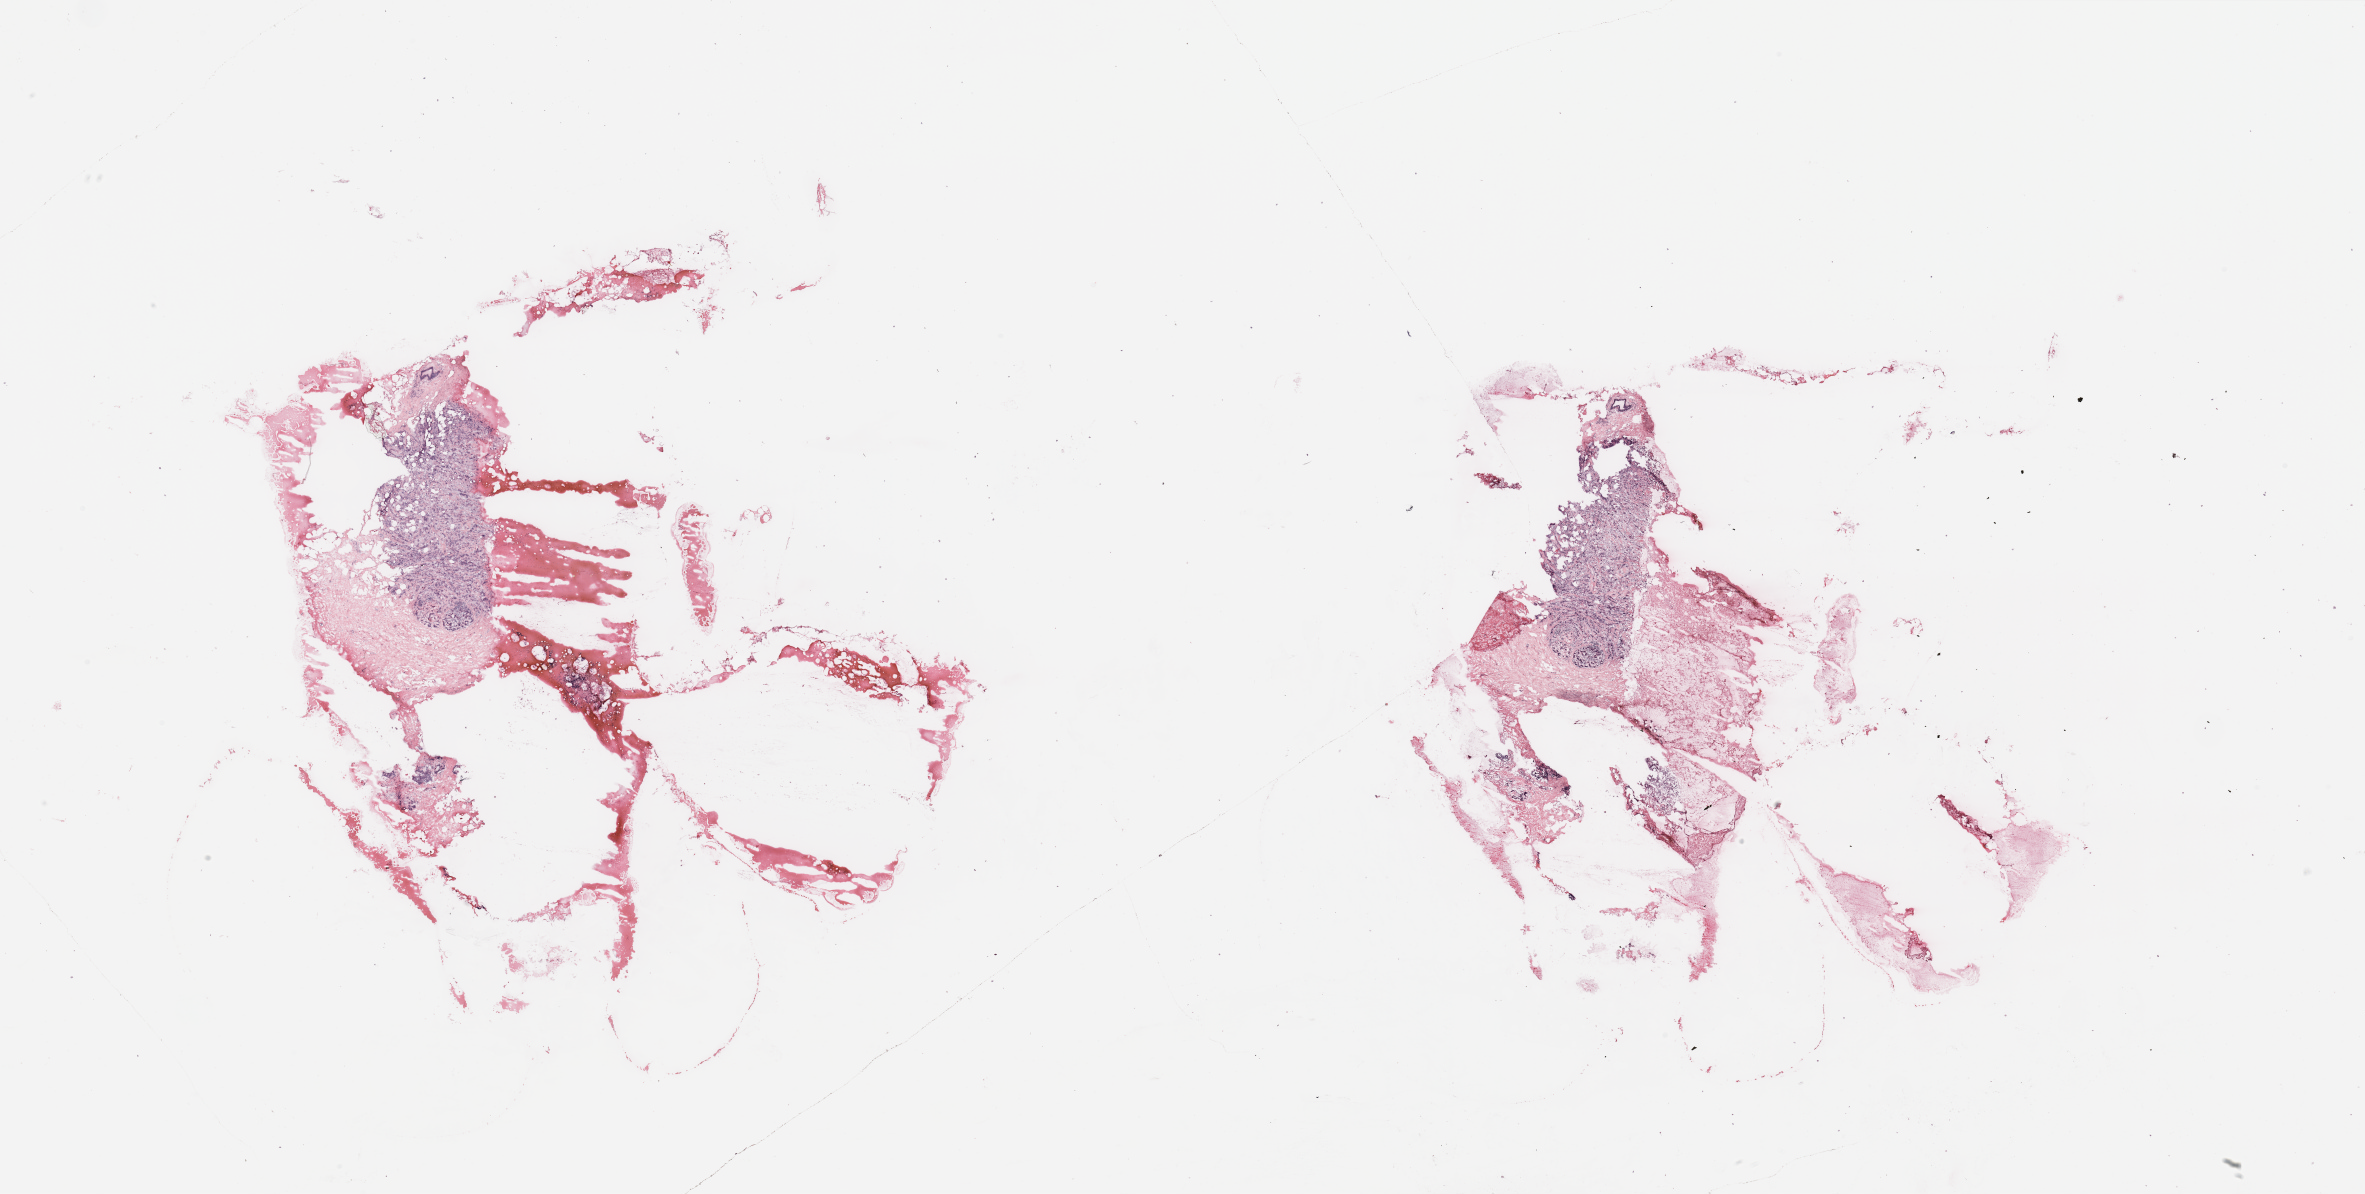
H&E whole-slide image, a low-resolution overview of the entire scanned area, about 37.4 x 18.9 mm (from a 20x scan). Breast, tissue type not recorded.
- patient diagnosis (cohort enrolment): breast cancer (breast)